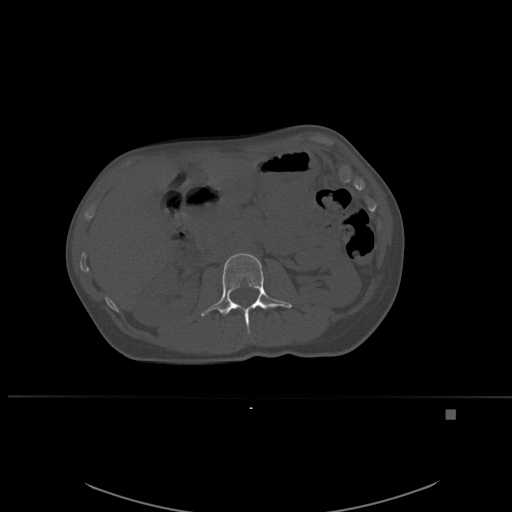
CT including the spine, one axial slice. Position 239 of 537 along the scan axis. Bone window (W 1800 / L 400 HU). 1.5 mm slice thickness. 512 × 512 image matrix, field of view 440 × 440 mm. Female patient, age 45 years. Case-level facts recorded for this patient, not image findings: primary cancer: lung.
Annotated regions visible in this slice (semi-automatic segmentation, software-assisted and operator-edited):
- L2 vertebra: bounding box [x1, y1, x2, y2] px = [201, 253, 292, 334]